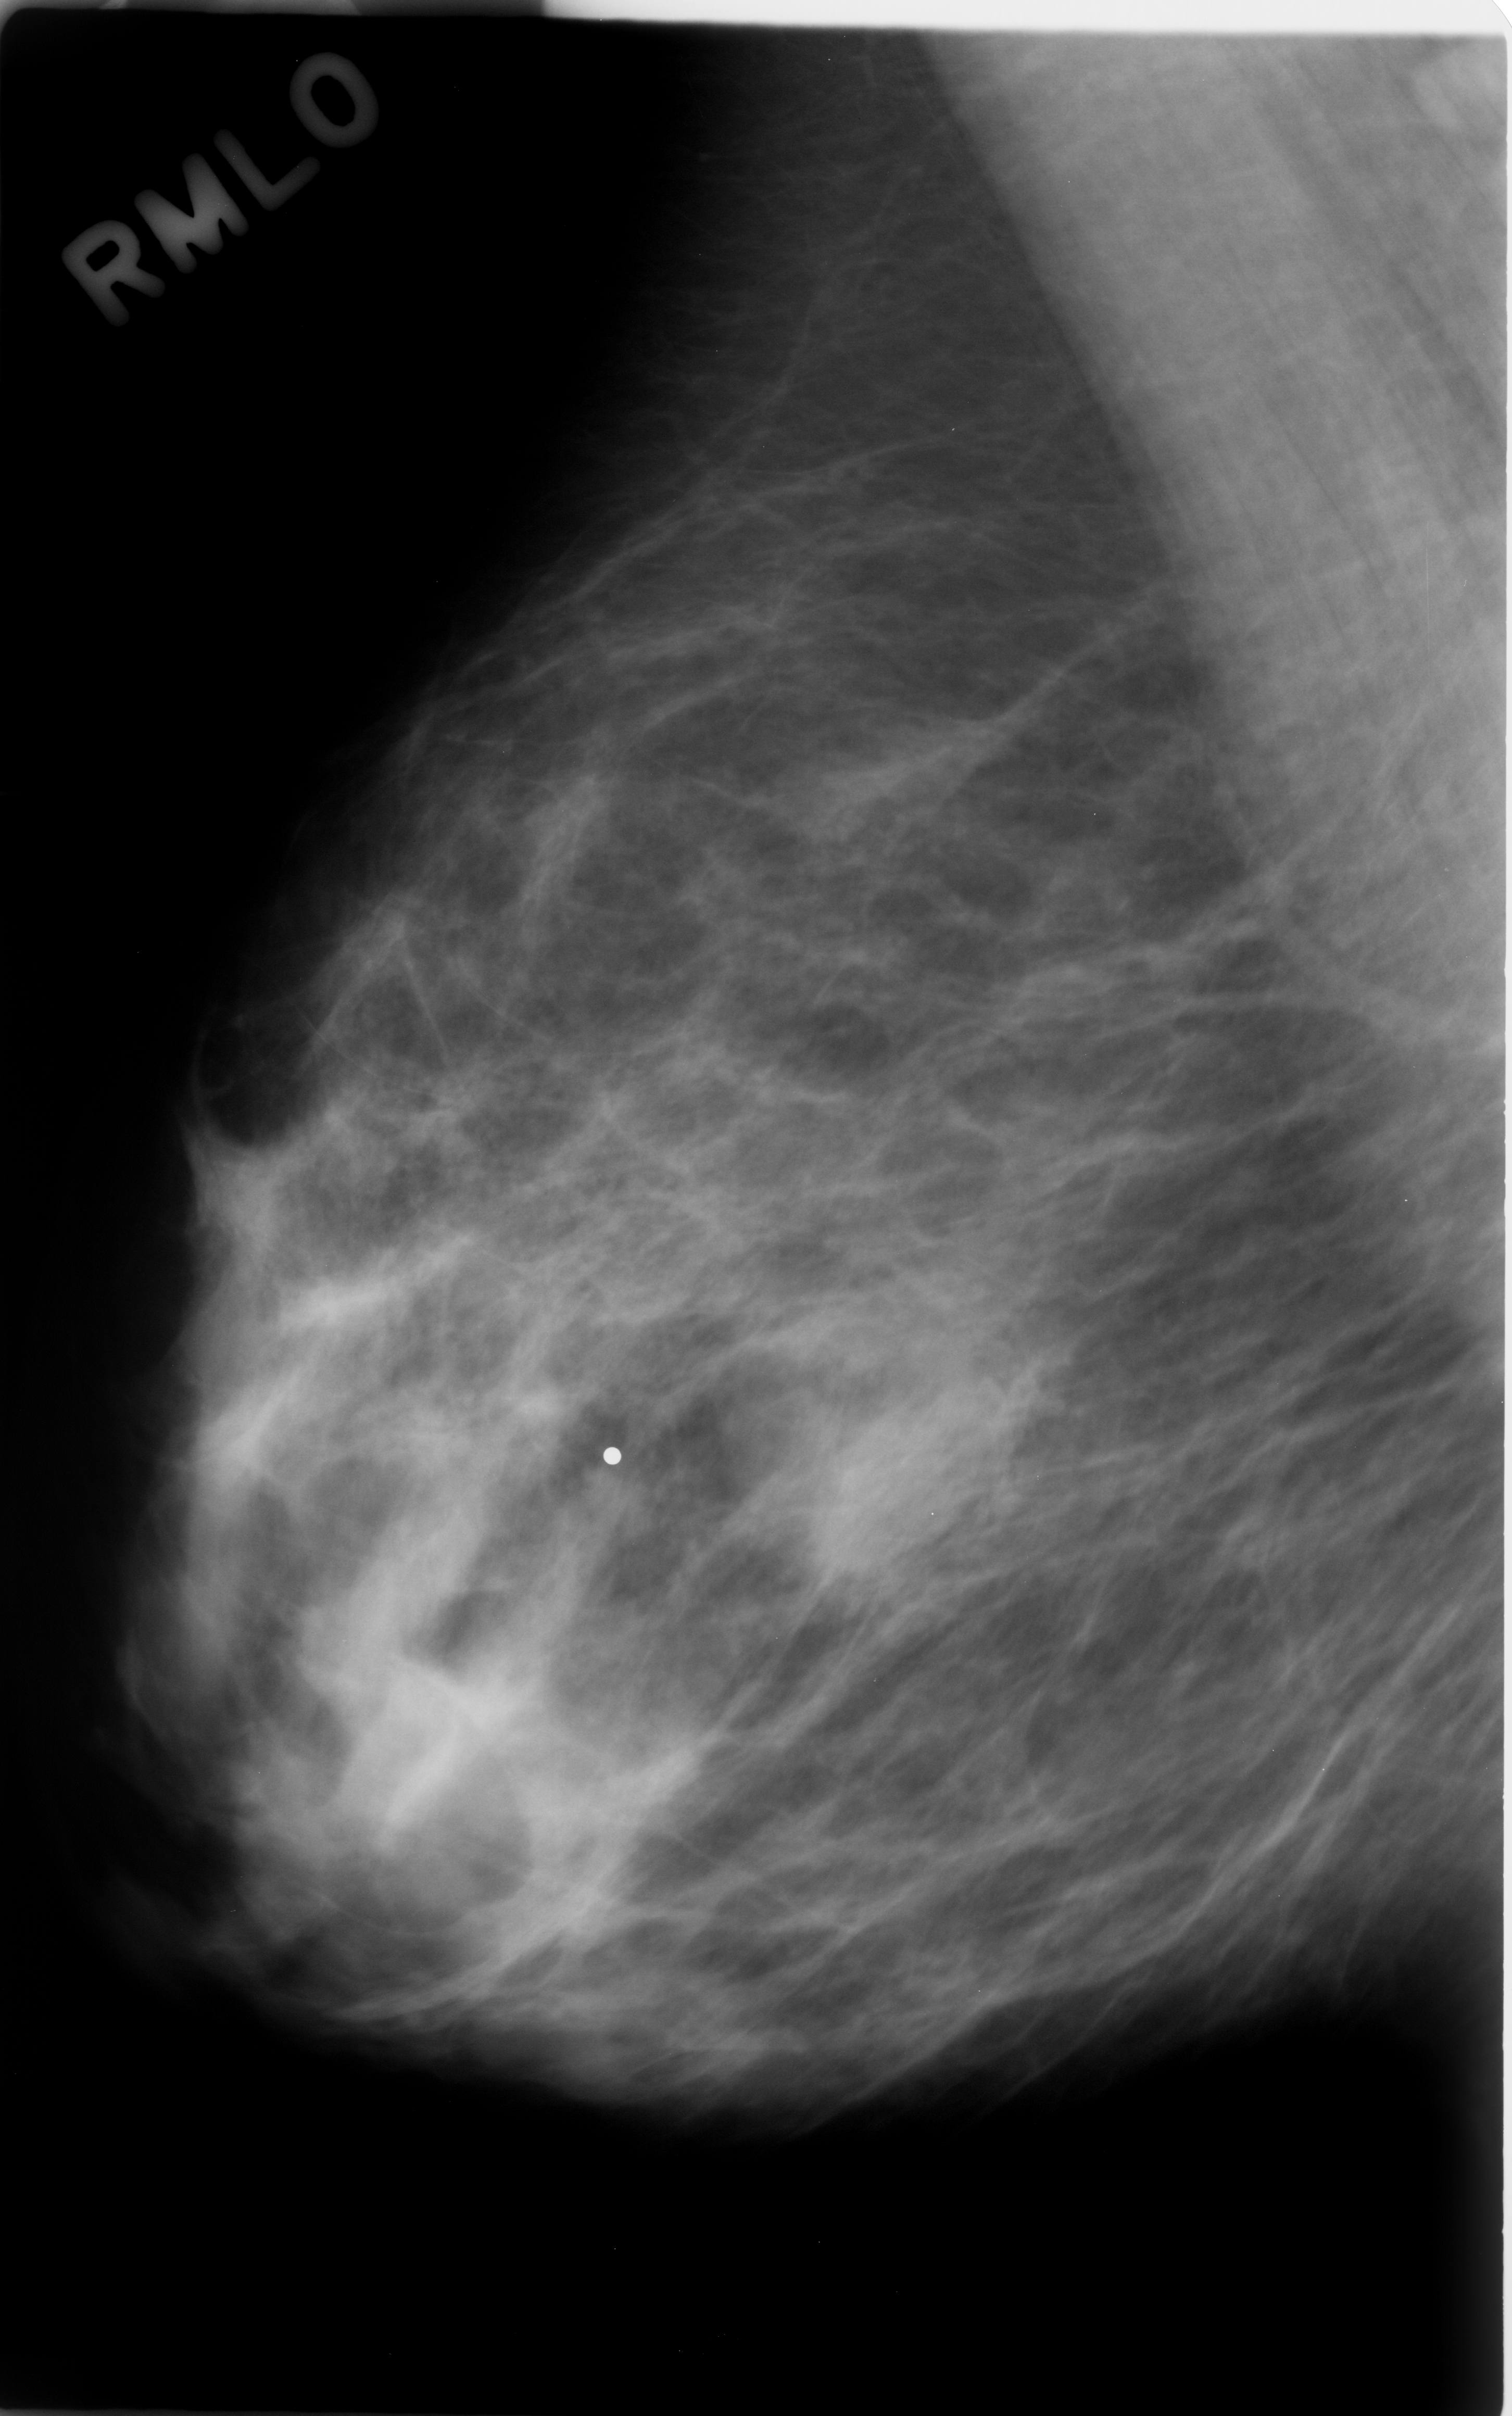
Scanned film-screen mammogram; right breast; MLO view.
- Finding: mass, shape oval, margins obscured; BI-RADS assessment category 4; pathology (as recorded): benign.